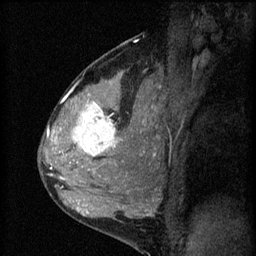
Breast MRI (dynamic contrast-enhanced), one sagittal slice; slice 39 of 60 in the series (ordered by position); 3 images stored at this slice position (order not interpretable as contrast timing); 1.5 T; TE 4.2 ms, TR 8.2 ms; 2 mm slice thickness; 256 × 256 image matrix. Patient: female, 37 years.
Outlined on this slice (semi-automatically segmented with operator editing):
- analysis volume of interest (the breast-tissue region the enhancement analysis was run in; not a lesion): box from (x=53, y=78) to (x=140, y=181) px
- tumour enhancement mask (voxels above the 70 % enhancement threshold inside the analysis volume of interest): (x=53, y=102)–(x=120, y=181)